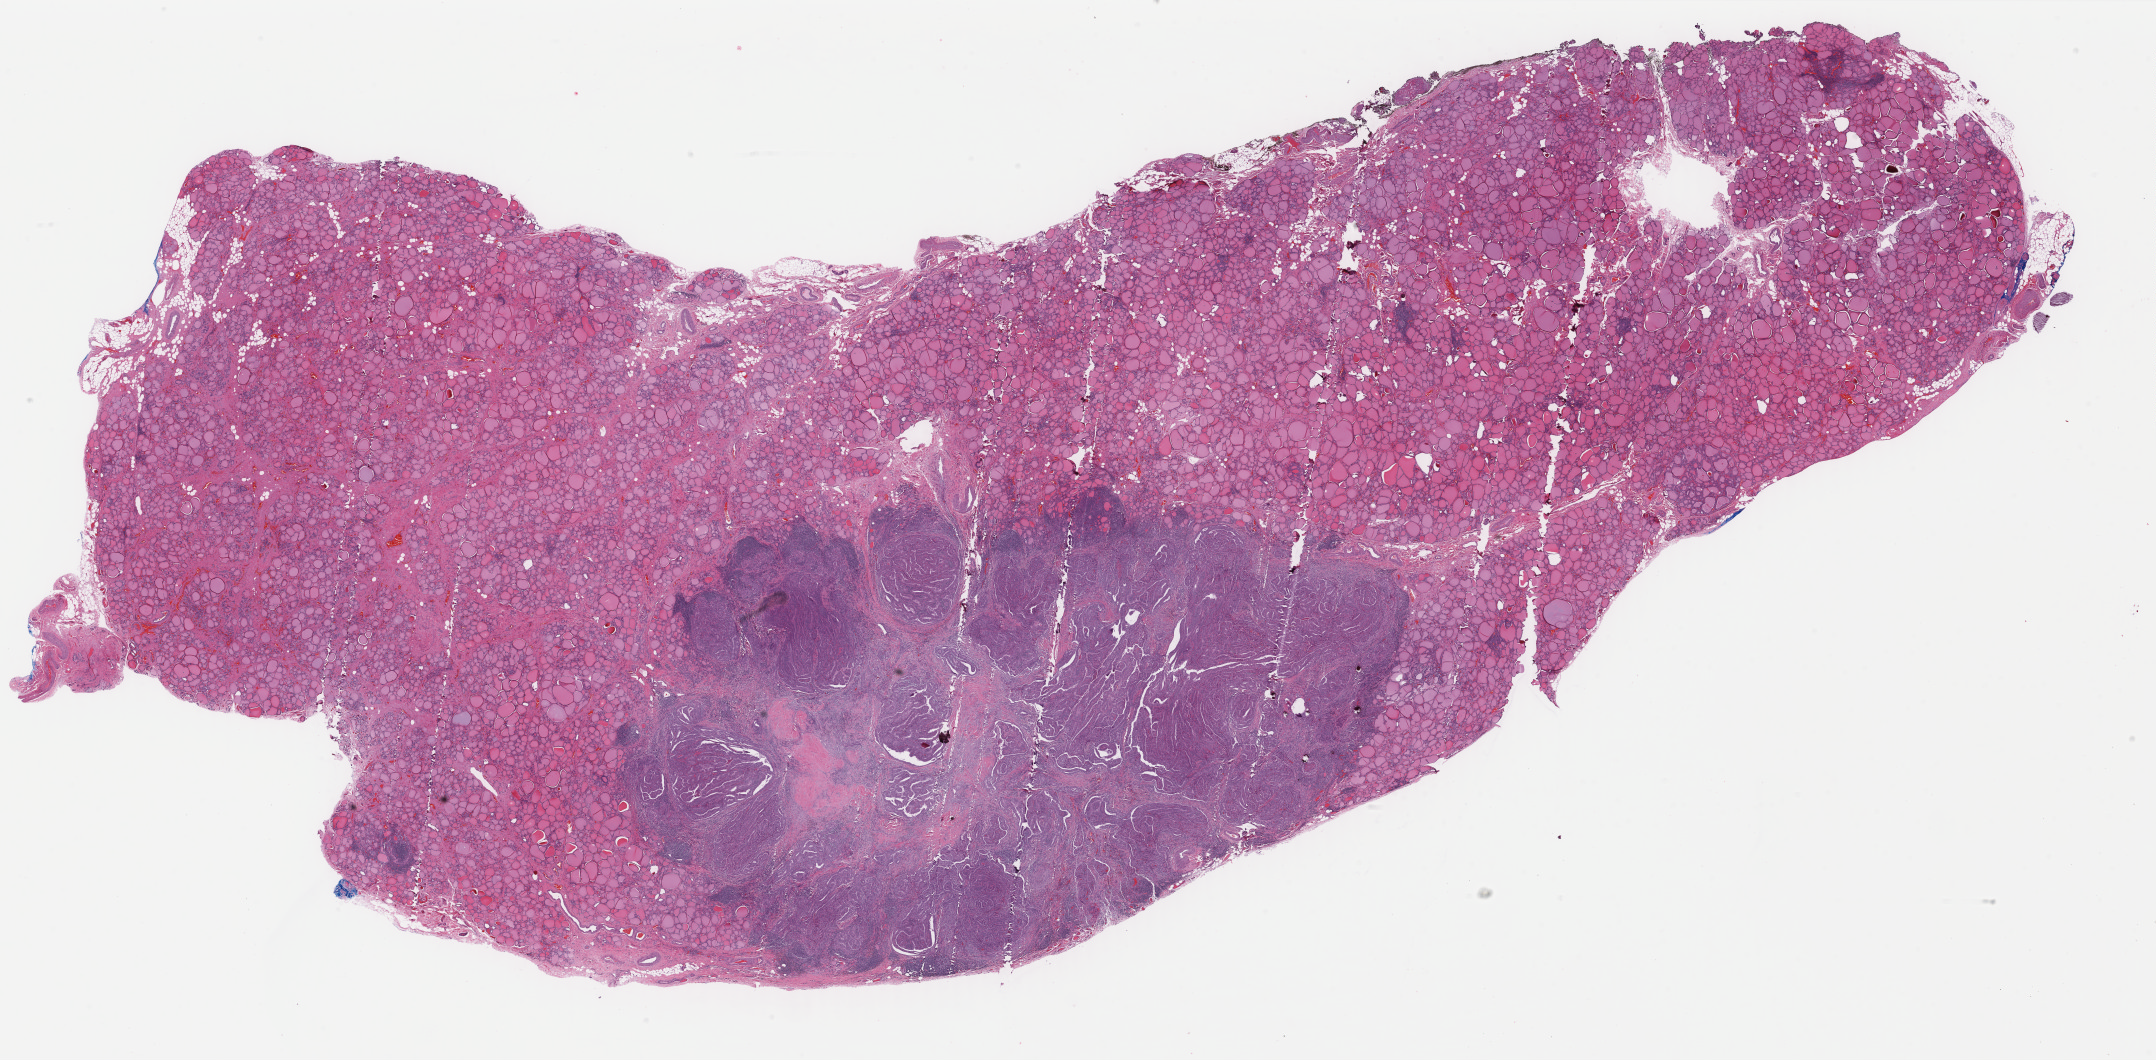
Whole-slide histology image, H&E, a low-resolution overview of the entire scanned area, about 34.2 x 16.8 mm; FFPE section; sample: primary tumour, thyroid. Male patient; age at initial diagnosis 85 years.
Diagnosis: Papillary carcinoma, columnar cell (thyroid gland).